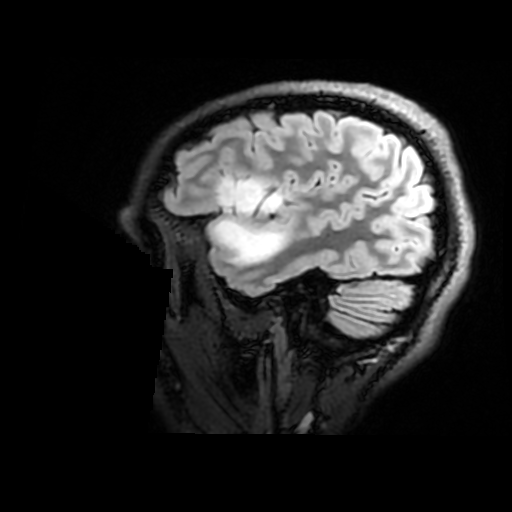
Brain MRI from a brain-tumour surgery series, one sagittal slice; position 136 of 176 along the scan axis; T2 FLAIR; 1 mm slice thickness; 512 × 512 image matrix, field of view 240 × 240 mm. Case-level facts recorded for this patient, not image findings: histopathology: Astrocytoma; WHO grade: 2; IDH mutation: yes; tumour location: Right Insular.
Annotated regions visible in this slice (manually delineated by an expert):
- tumour: bounding box (x1, y1, x2, y2) in pixels: (216, 179, 290, 266)